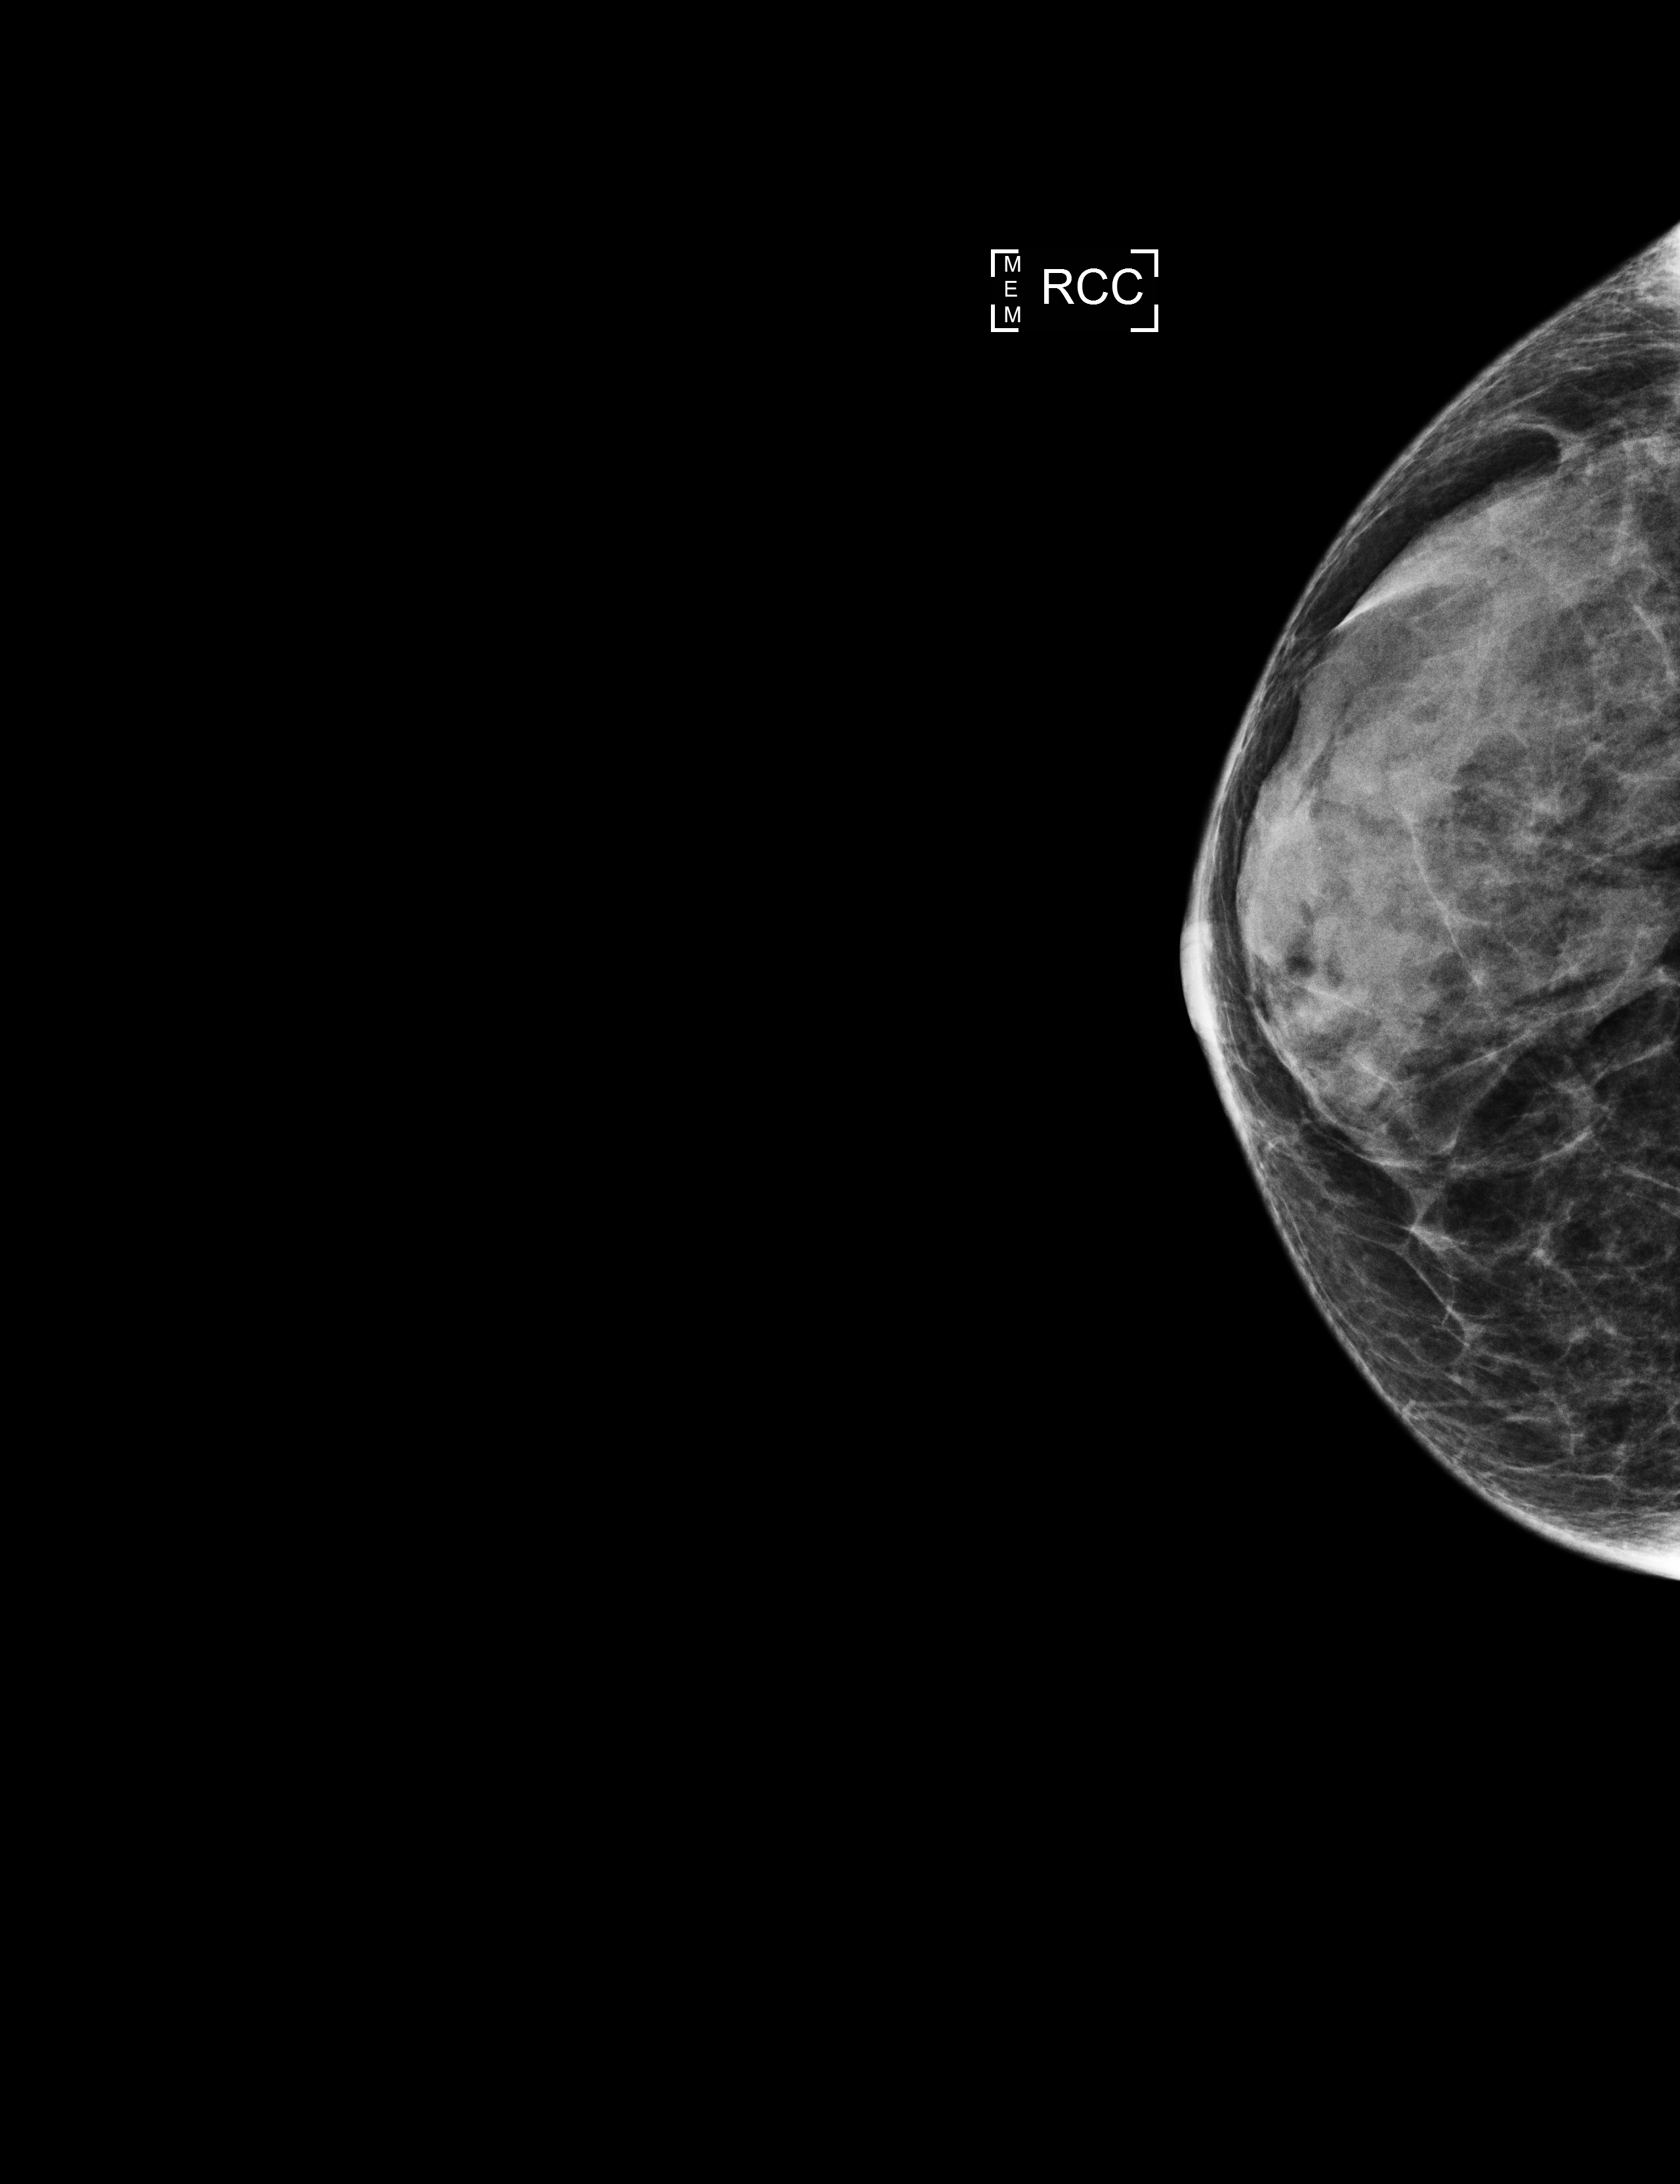
Annual screening mammography examination; compressed breast thickness 24 mm. Female patient, age 60 years.
Image type: full-field digital mammogram. Breast: right. Projection: craniocaudal (CC) view.